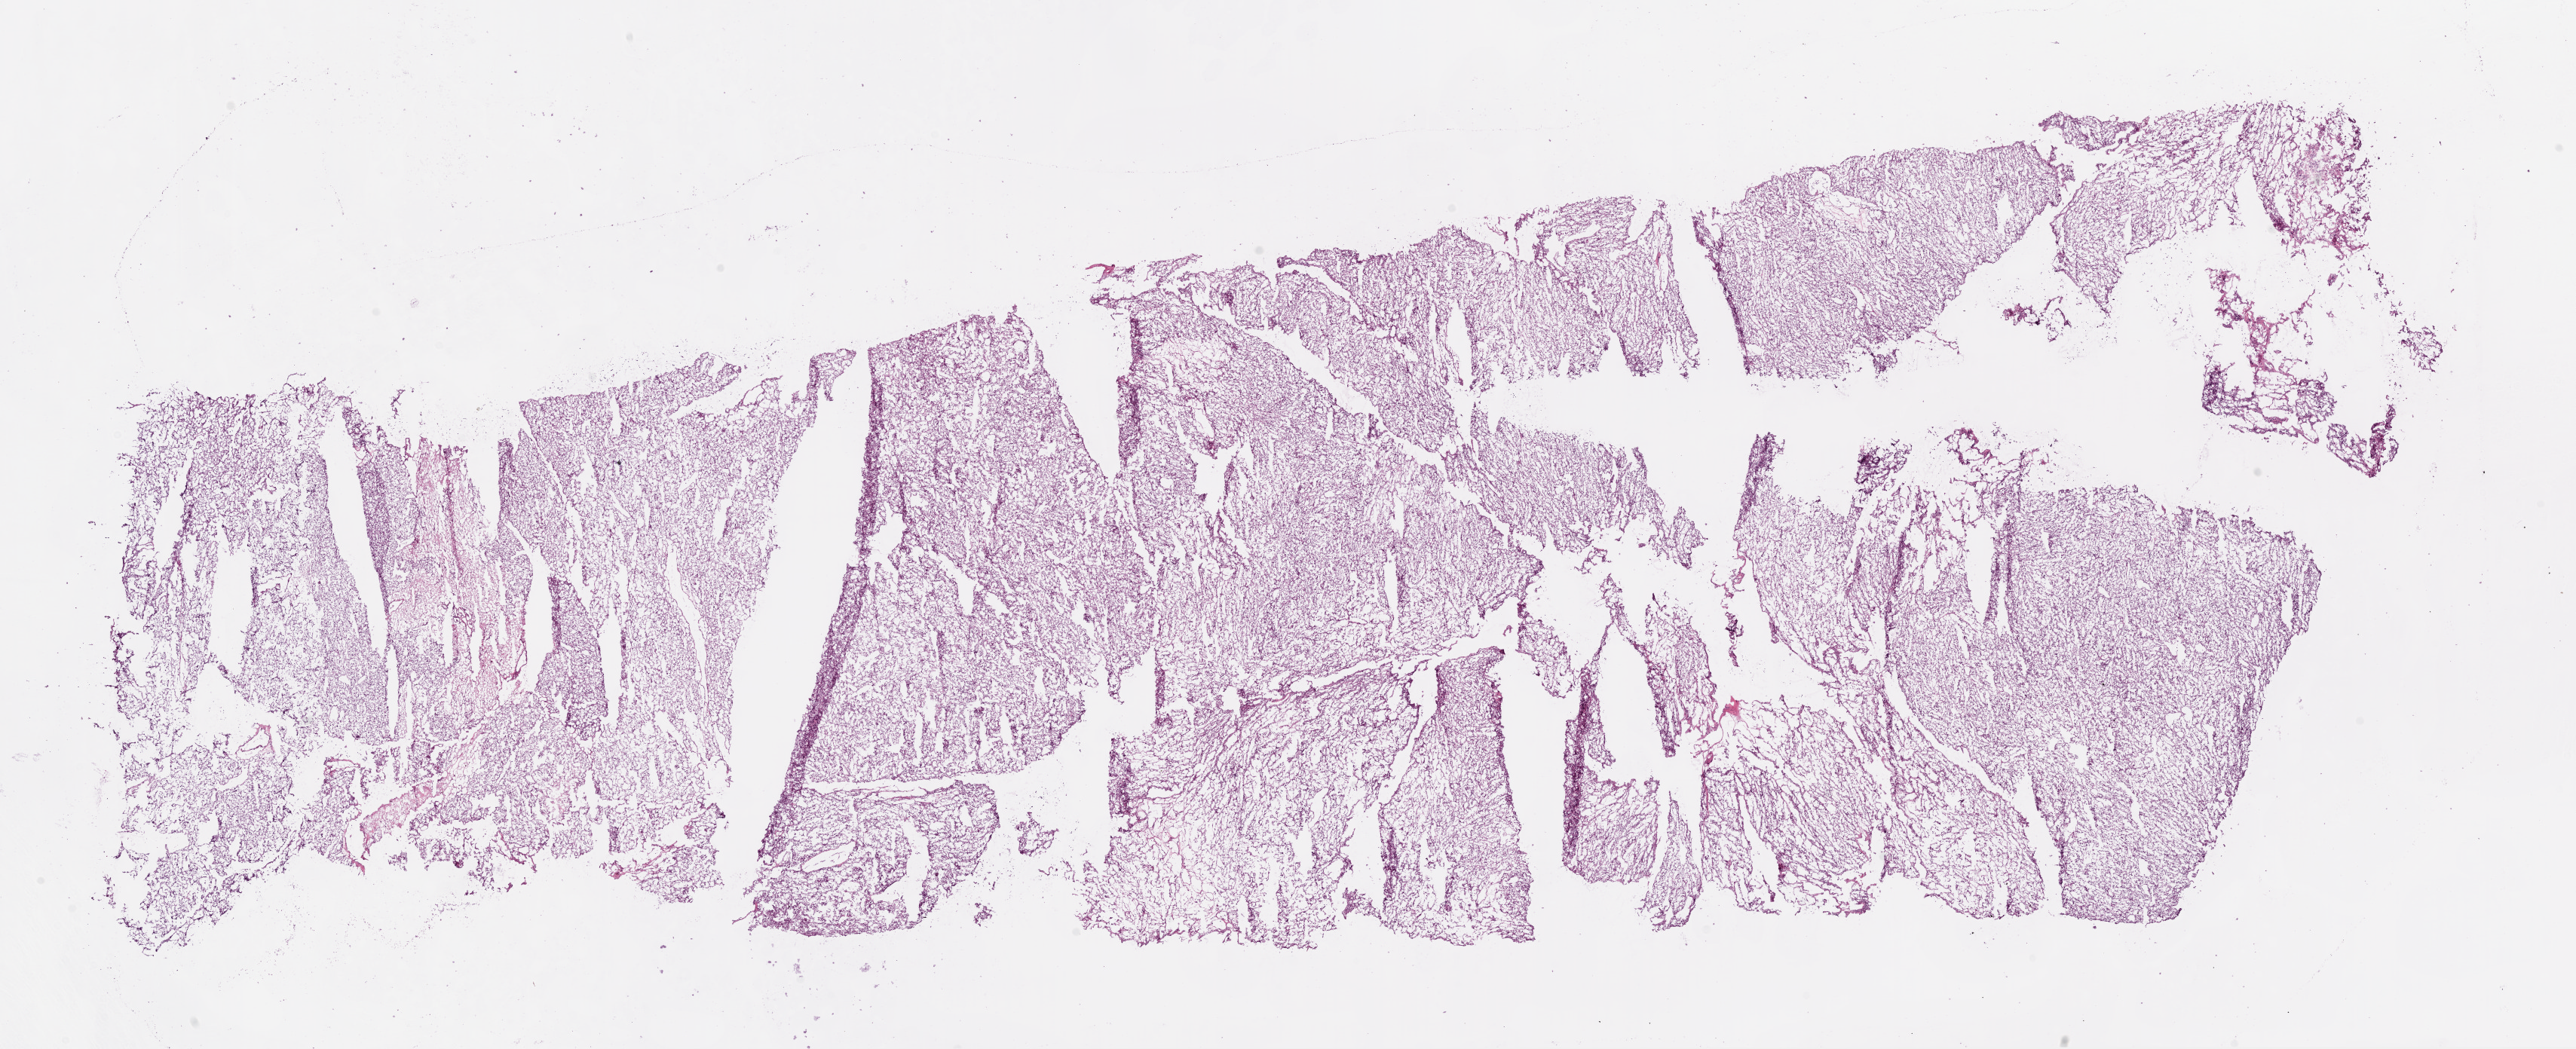
Digitized Hematoxylin and eosin (H&E) stained tissue section (whole slide) — a low-resolution overview of the entire scanned area, about 27.6 x 11.2 mm, frozen section from the top of the tissue portion, primary tumour sample from the kidney. Male patient; age at initial diagnosis 78 years. Histologic grade: G3 (poorly differentiated). Pathologist review of this section (percent, as recorded): tumour cells 92%, tumour nuclei 85%, normal cells 0%, stromal cells 8%, necrosis 0%.
Histologic diagnosis: Clear cell adenocarcinoma, NOS. AJCC pathologic stage: I.